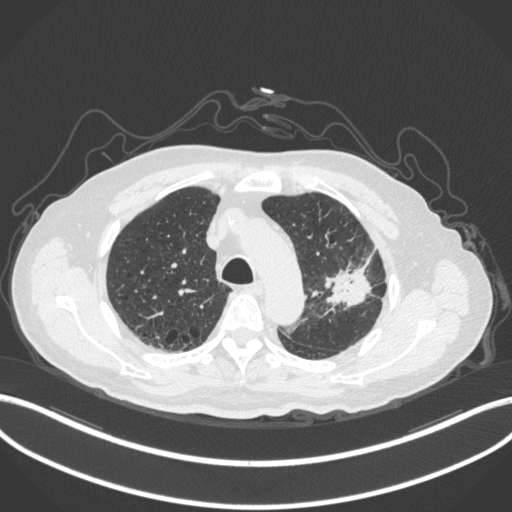
Chest CT, one axial slice. Position 222 of 331 along the scan axis. 120 kVp. Lung window (W 1500 / L -600 HU). 512 × 512 image matrix, field of view 400 × 400 mm. Male patient, age 79 years. Case-level facts recorded for this patient, not image findings: clinical TNM (as recorded): T2a N1 M1.
Outlined on this slice (rectangle marked by the reading radiologist):
- lung tumour (recorded histology: adenocarcinoma): box from (x=323, y=262) to (x=376, y=307) px